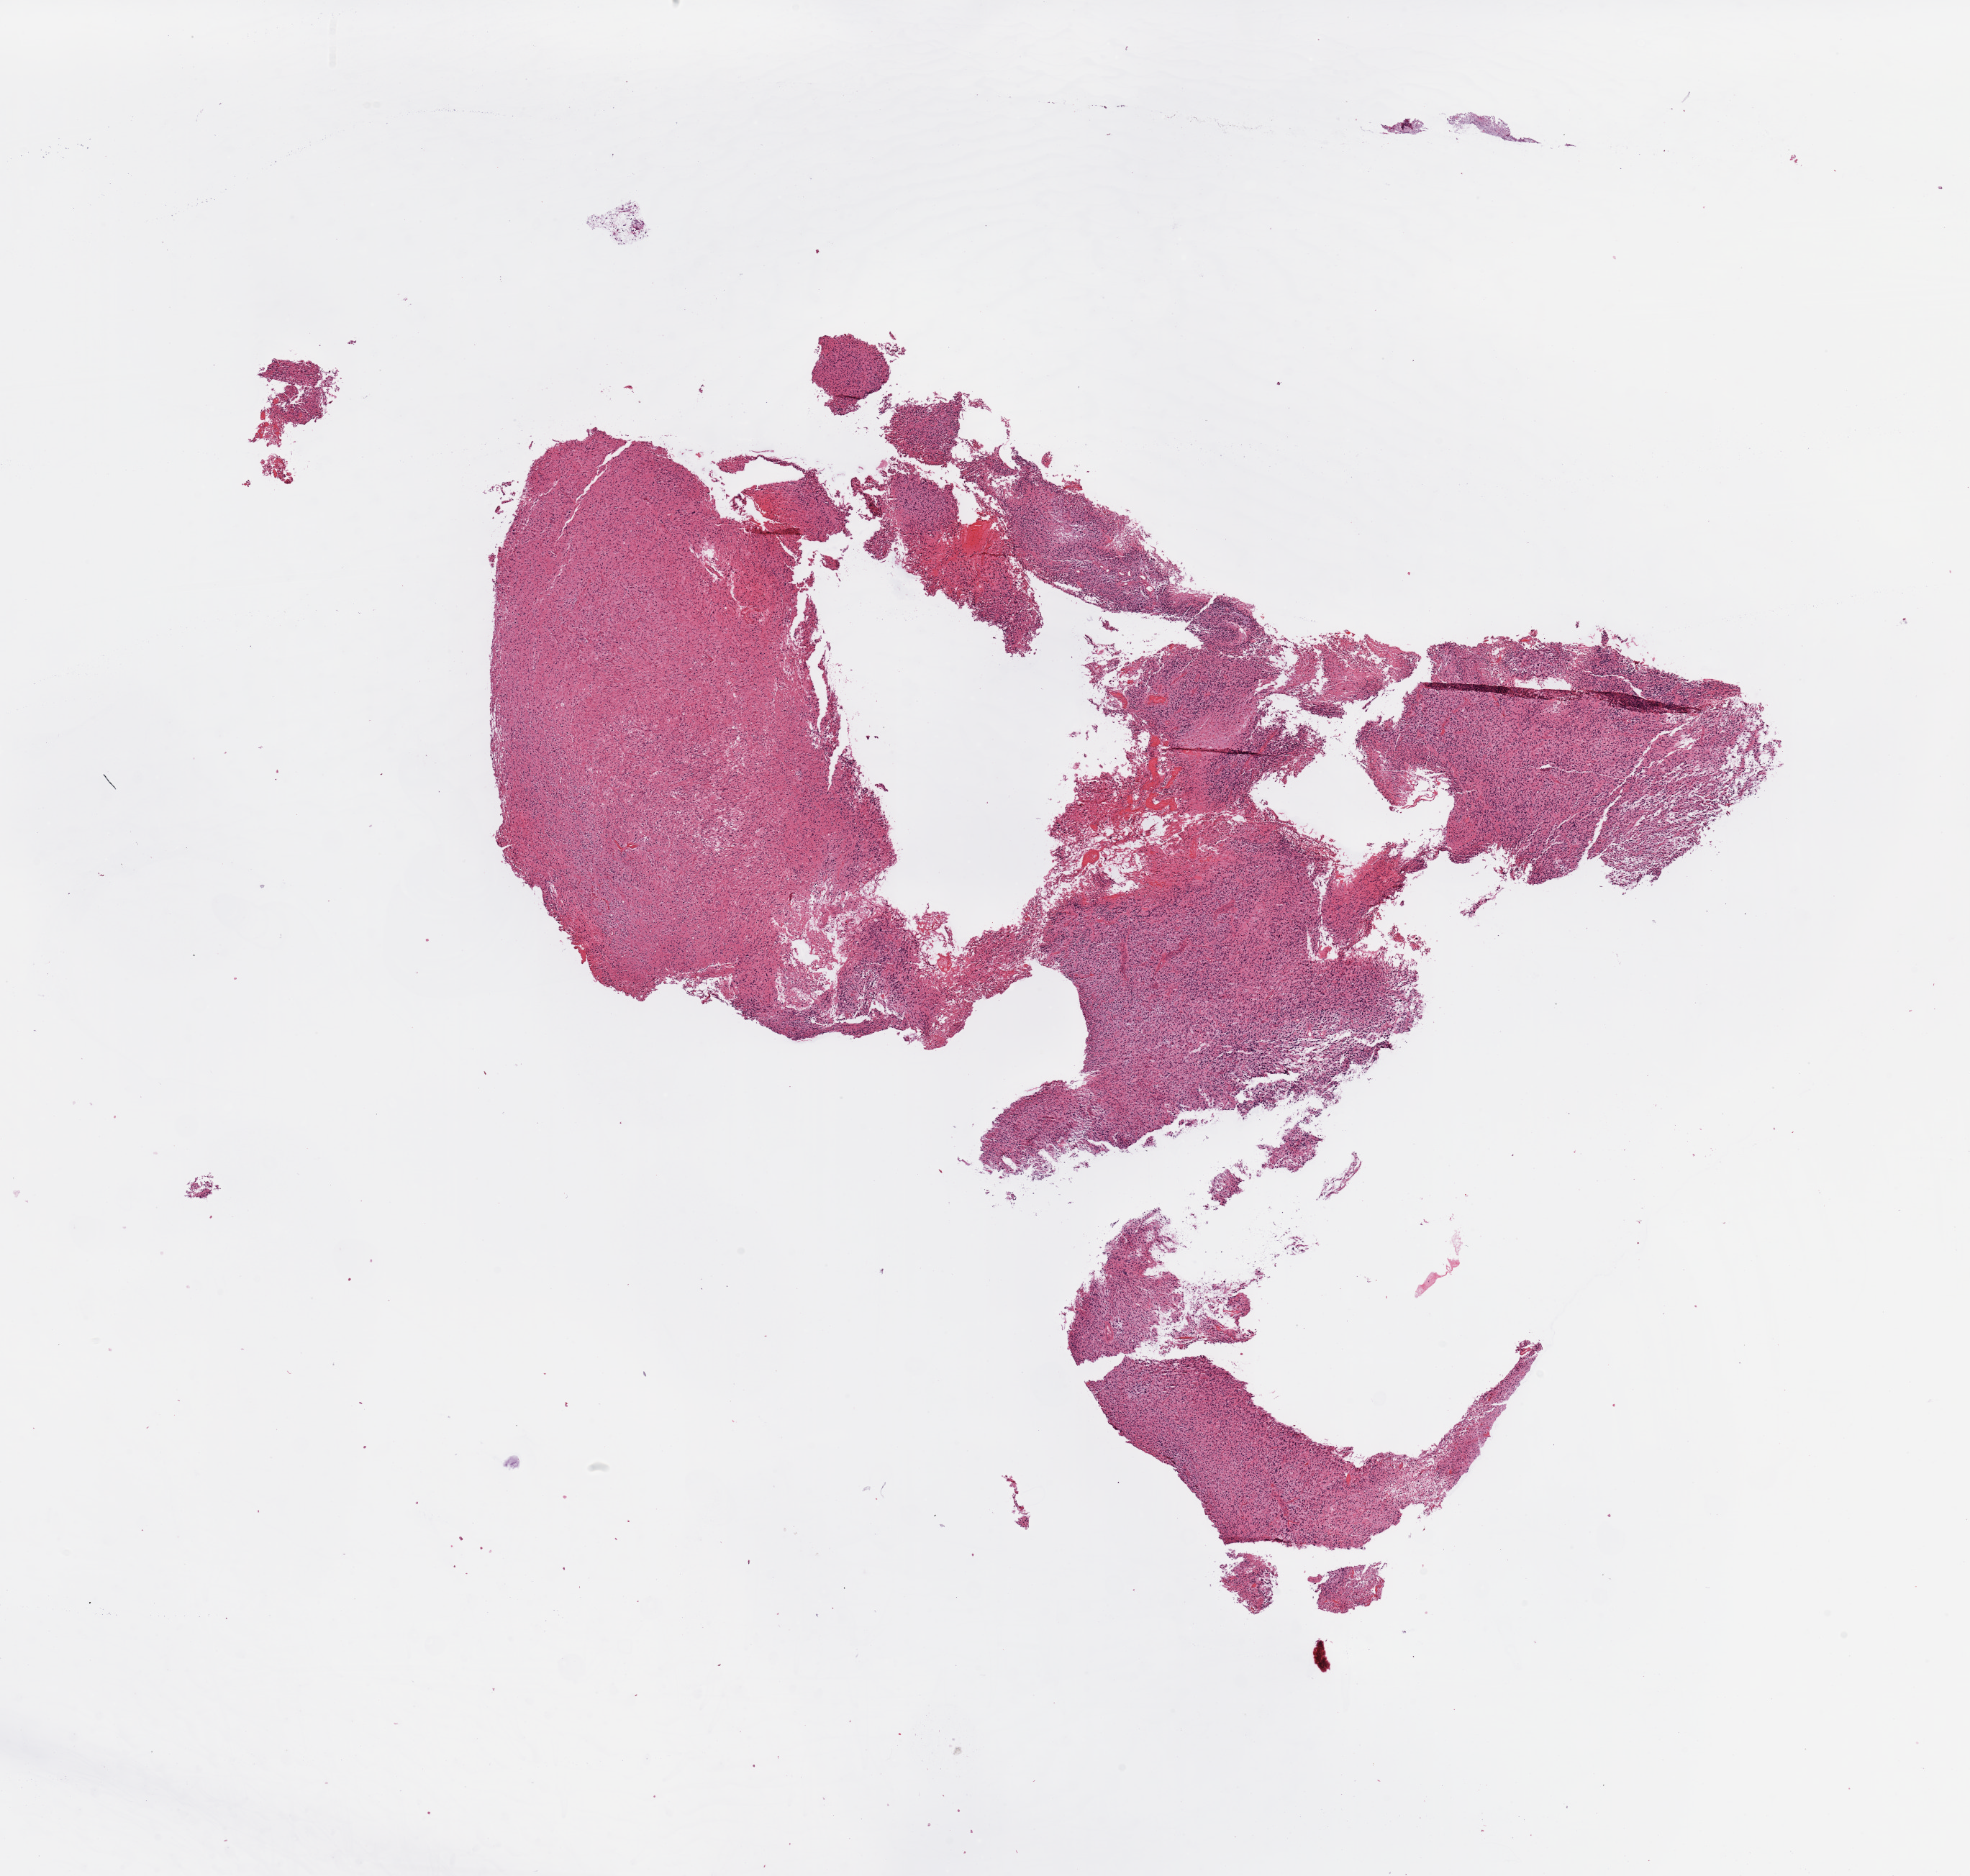
Whole-slide histology image, Hematoxylin and eosin (H&E) stained, a low-resolution overview of the entire scanned area, about 21.7 x 20.6 mm. Brain, tumour tissue. 70-year-old male patient.
Patient diagnosis (cohort enrolment): glioblastoma multiforme (brain). Primary tumour site (as recorded): parietal lobe.